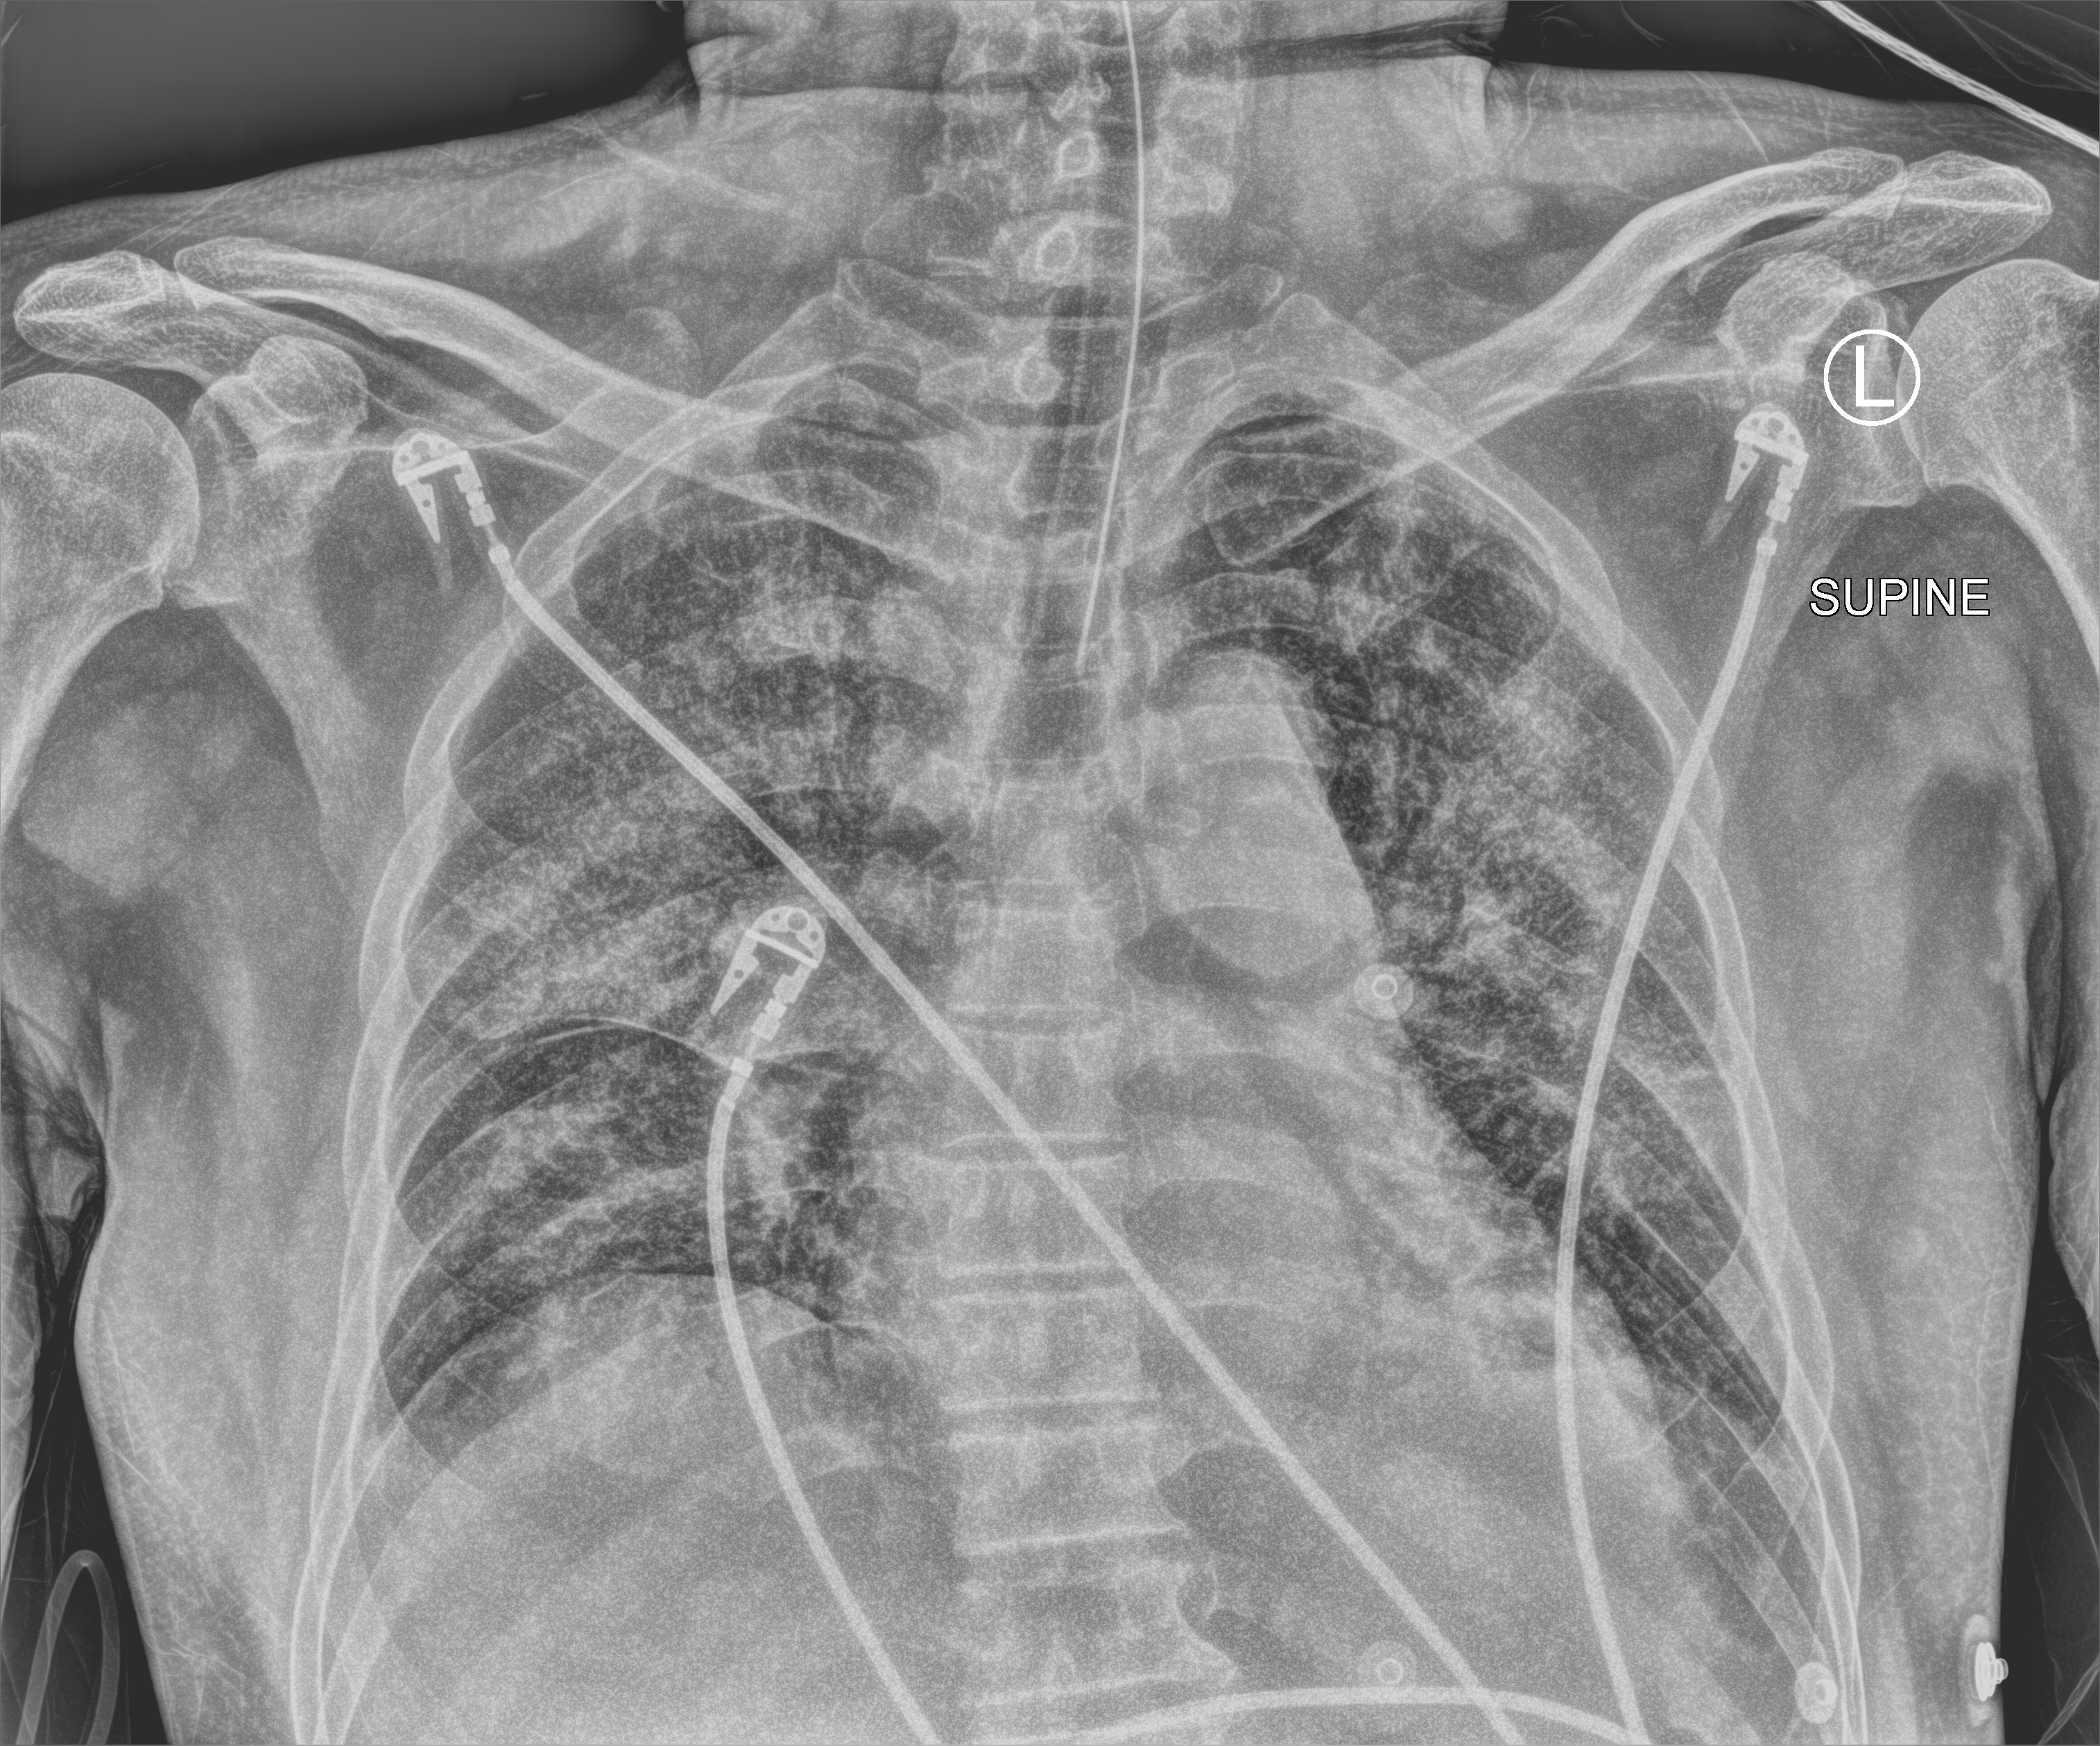
Chest X-ray (portable). Patient hospitalised with COVID-19; male, aged 60–74 years.
Hospital-stay facts (about this admission, not read from this image; timing relative to this image not recorded): other chronic lung disease (admission record): no; mechanically ventilated during this hospital stay: yes; length of hospital stay: 14 days.